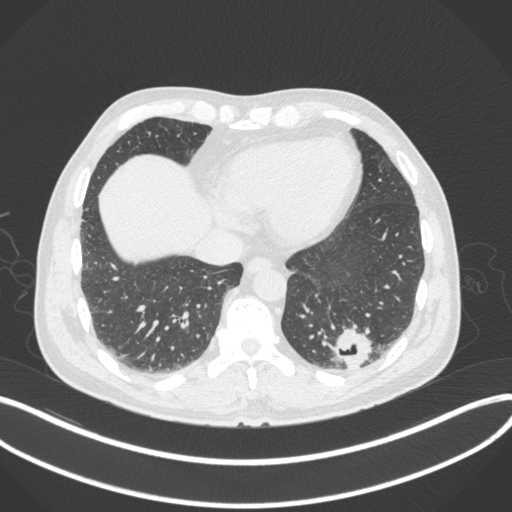
Chest CT, one axial slice. Position 74 of 313 along the scan axis. Reconstruction kernel B31f. 120 kVp. Lung window (W 1500 / L -600 HU). 1 mm slice thickness. 512 × 512 image matrix, field of view 400 × 400 mm. Male patient, age 54 years. Case-level facts recorded for this patient, not image findings: clinical TNM (as recorded): T1c N0 M1.
Annotated regions visible in this slice (bounding box drawn by a radiologist):
- lung tumour (recorded histology: adenocarcinoma): bounding box (x1, y1, x2, y2) in pixels: (334, 322, 373, 369)